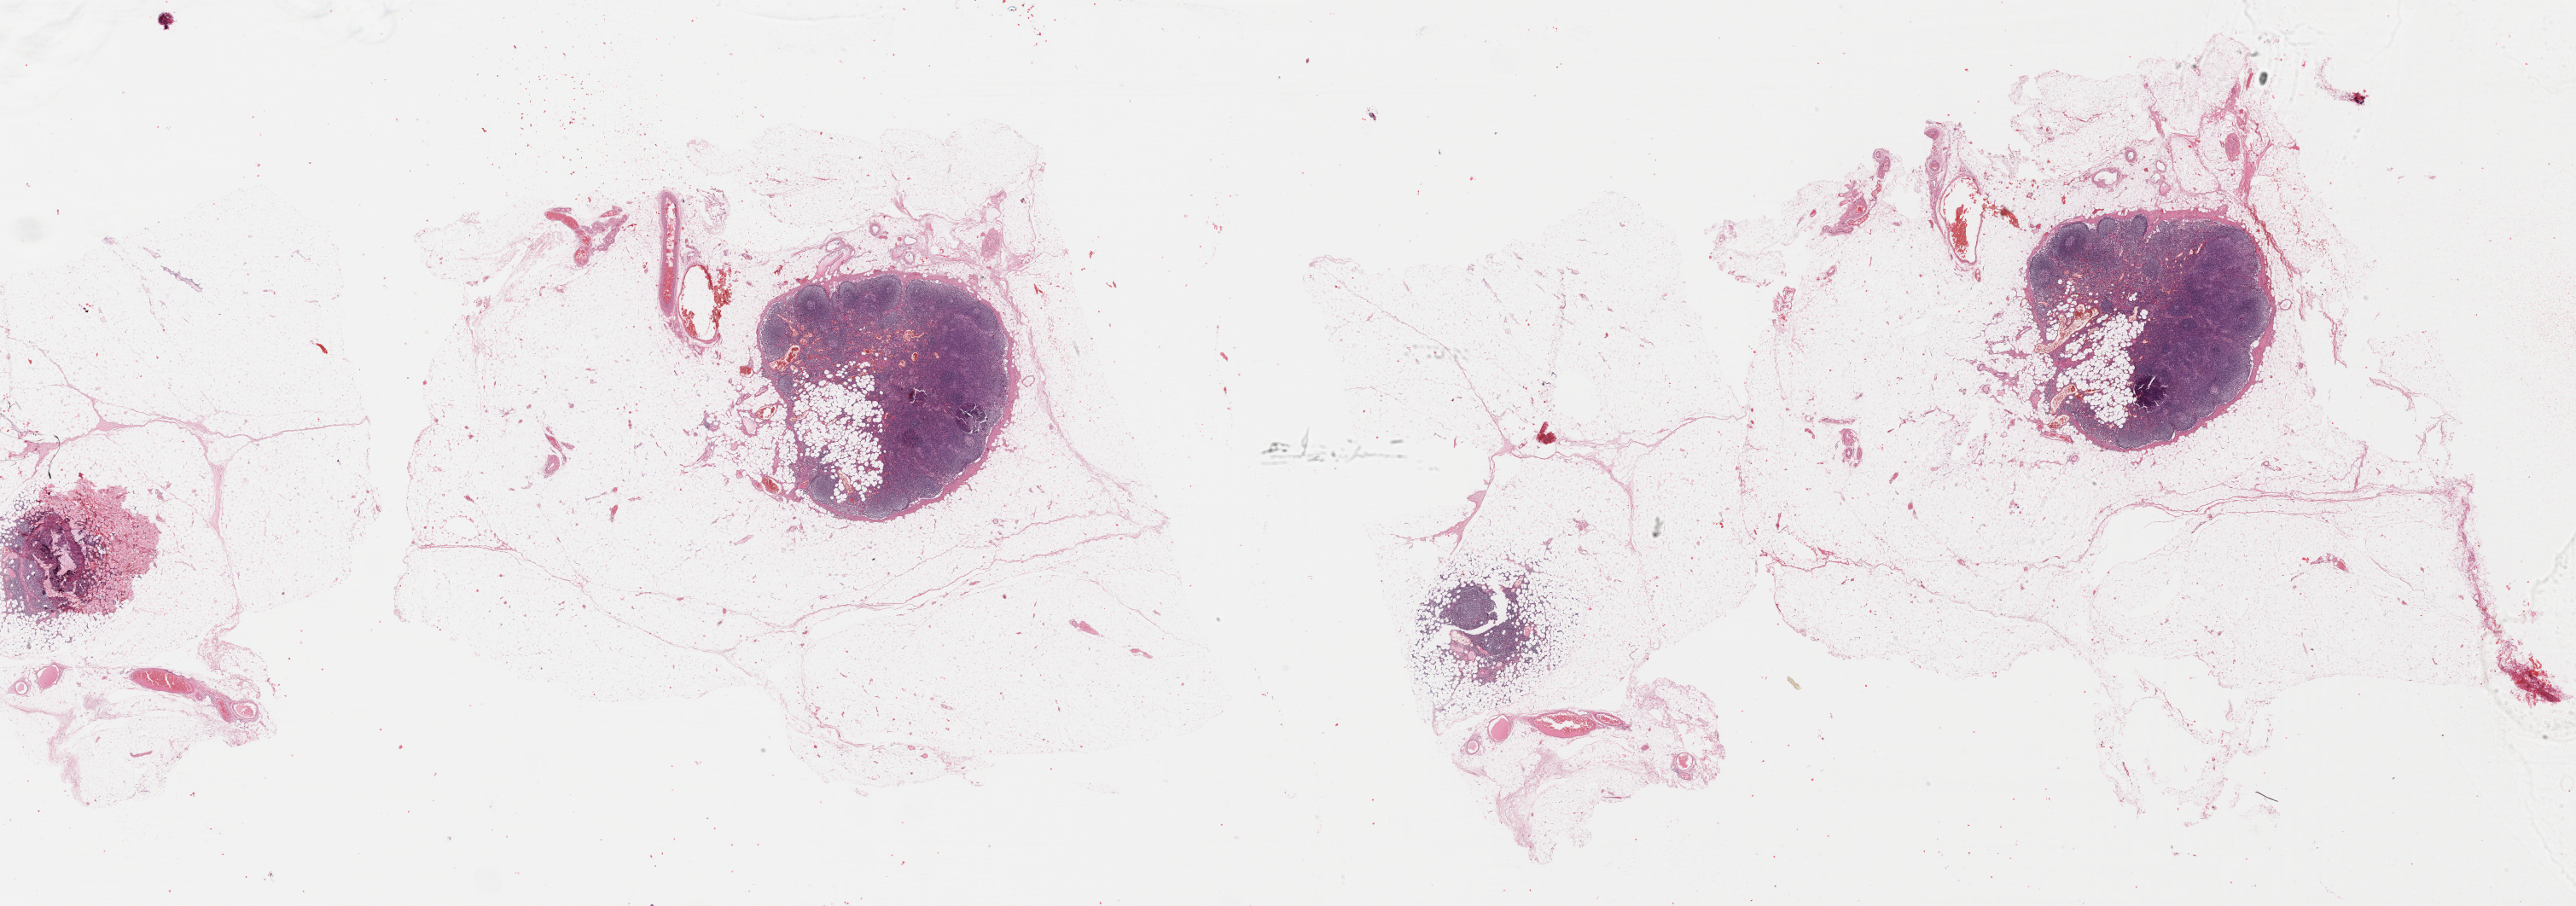
Digitized H&E tissue section (whole slide) — whole scanned area (about 47.5 x 16.7 mm) shown as a low-resolution overview; FFPE section; metastatic tumour sample, sampled site: lymph node. Male, age 65 years at initial diagnosis.
- this section: metastatic tumour tissue
- patient diagnosis: Malignant melanoma, NOS